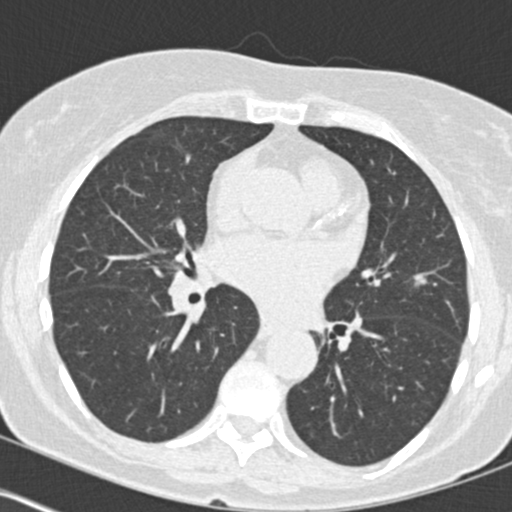
Low-dose screening chest CT, one axial slice; slice 84 of 160 in the series (ordered by position); reconstruction kernel B30f; 120 kVp; lung window (W 1500 / L -600 HU); 2 mm slice thickness; 512 × 512 image matrix, field of view 300 × 300 mm.
Annotated regions visible in this slice (outlined manually by an expert reader):
- lesion 1 (tumor, upper lobe of left lung): bounding box <415,274,426,284> (left, top, right, bottom; pixels)